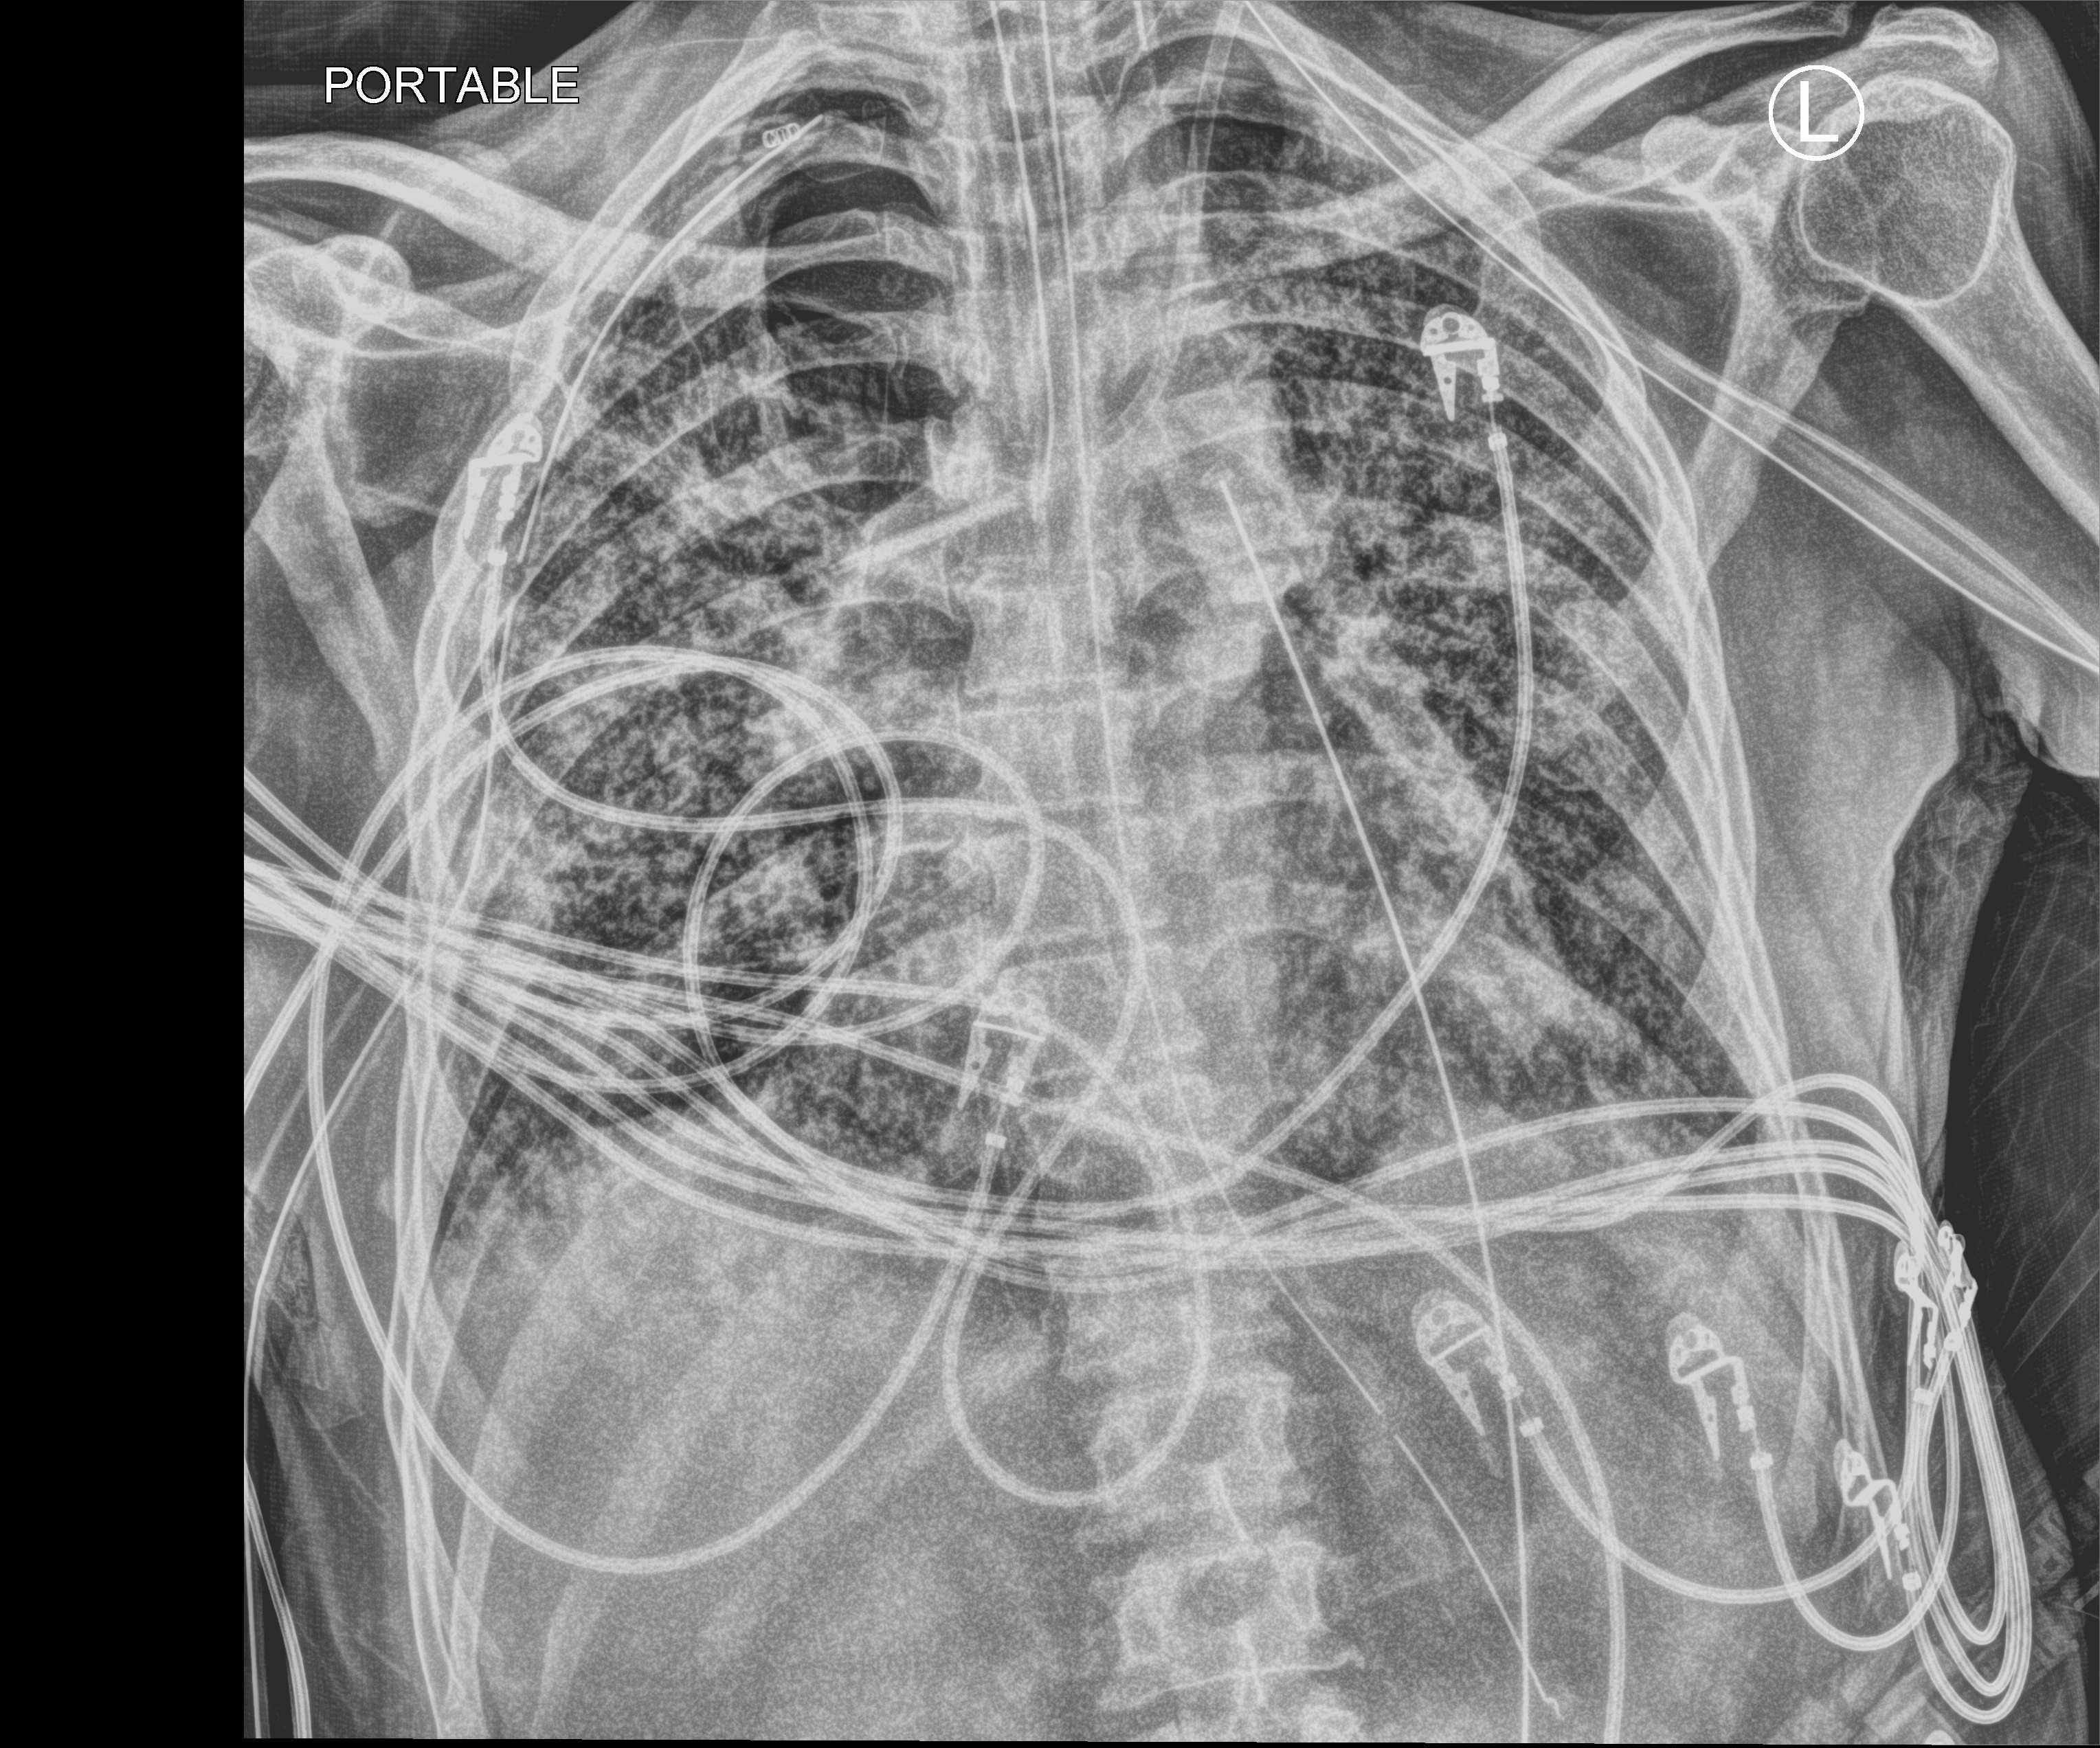
Portable chest radiograph; anteroposterior (AP) projection. Patient hospitalised with COVID-19; male, aged 60–74 years.
From the hospital-stay record, not from the radiograph (when in the stay this image was taken is not recorded):
- smoking status (admission record): never
- mechanically ventilated during this hospital stay: yes
- other chronic lung disease (admission record): yes